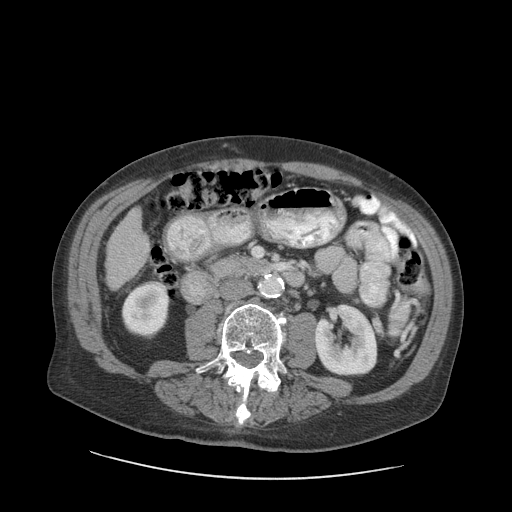
Contrast-enhanced abdominal CT (liver protocol), one axial slice. Slice 25 of 89 in the series (ordered by position). Soft-tissue window (W 400 / L 40 HU). 2.5 mm slice thickness. 512 × 512 image matrix, field of view 420 × 420 mm. Case-level facts recorded for this patient, not image findings: diagnosis: hepatocellular carcinoma (patient treated with transarterial chemoembolisation; whether this scan precedes or follows treatment is not stated here); TNM stage (as recorded): Stage-I; Child-Pugh class: A; tumour differentiation: moderately differentiated; tumour nodularity: uninodular.
Structures marked on this image (semi-automatically segmented with operator editing):
- liver parenchyma outside the tumour (the mass and vessels are separate outlines, so this box may not span the whole liver): bounding box (x1, y1, x2, y2) in pixels: (106, 208, 150, 289)